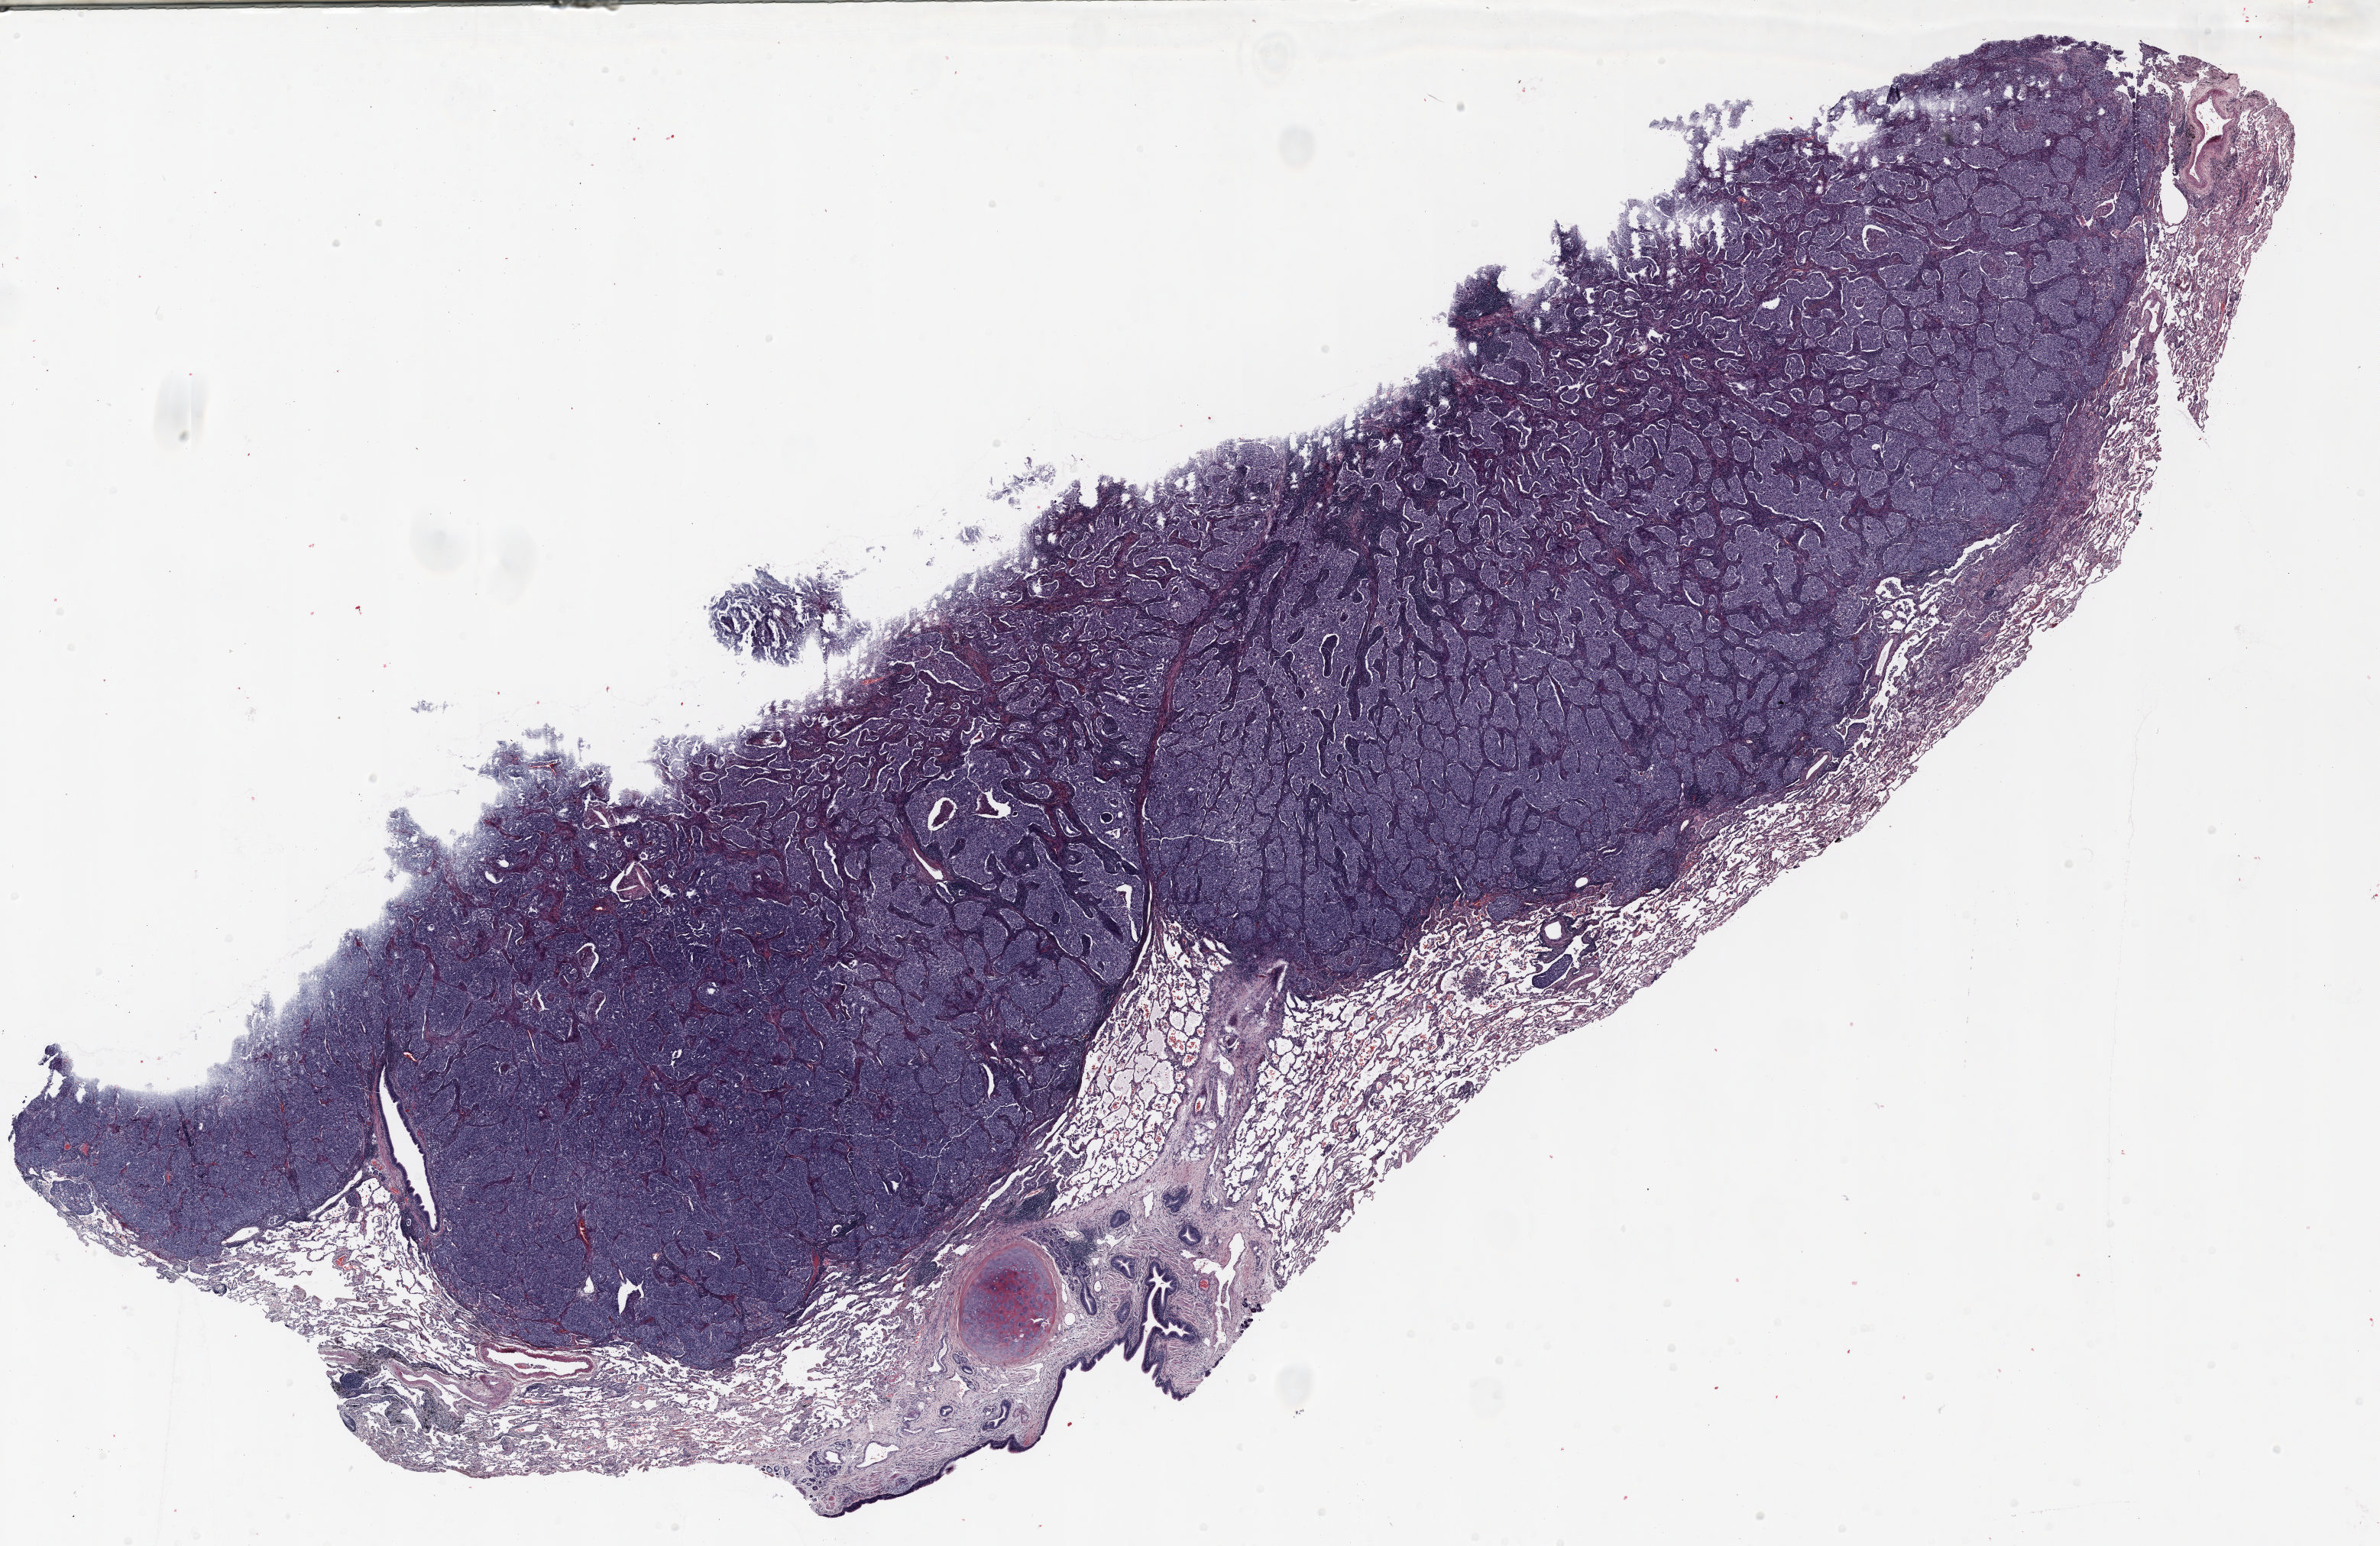
Whole-slide histology image, Hematoxylin and eosin (H&E) stained — shown as a low-resolution overview of the whole scanned area (about 25.0 x 16.3 mm, slide scanned at 20x). Formalin-fixed paraffin-embedded (FFPE) section. Lung. Male, age 72 at enrolment. Former smoker at enrolment. Grade: moderately differentiated (G2).
Participant's lung-cancer diagnosis: Adenosquamous carcinoma. Primary tumour location (clinical record): right upper lobe. Stage (AJCC 6th edition): IIIA. Tumour size (pathology): 53 mm.